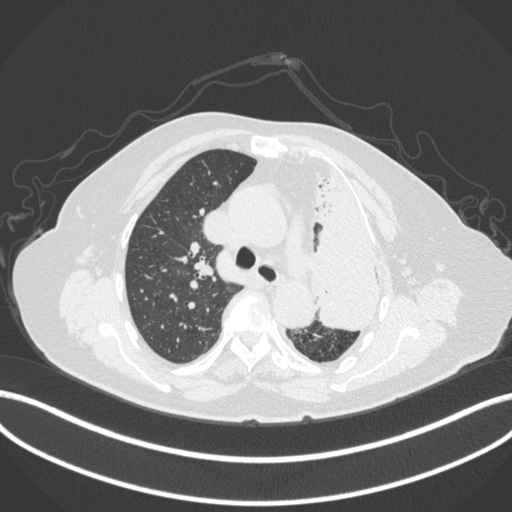
Chest CT, one axial slice. Reconstruction kernel B31f. 120 kVp. Lung window (W 1500 / L -600 HU). 1 mm slice thickness. 512 × 512 image matrix. Patient: female, 75 years. Case-level facts recorded for this patient, not image findings: clinical TNM (as recorded): T3 N3 M1.
Outlined on this slice (bounding box drawn by a radiologist):
- lung tumour (recorded histology: adenocarcinoma): bounding box [x1, y1, x2, y2] px = [309, 159, 388, 331]